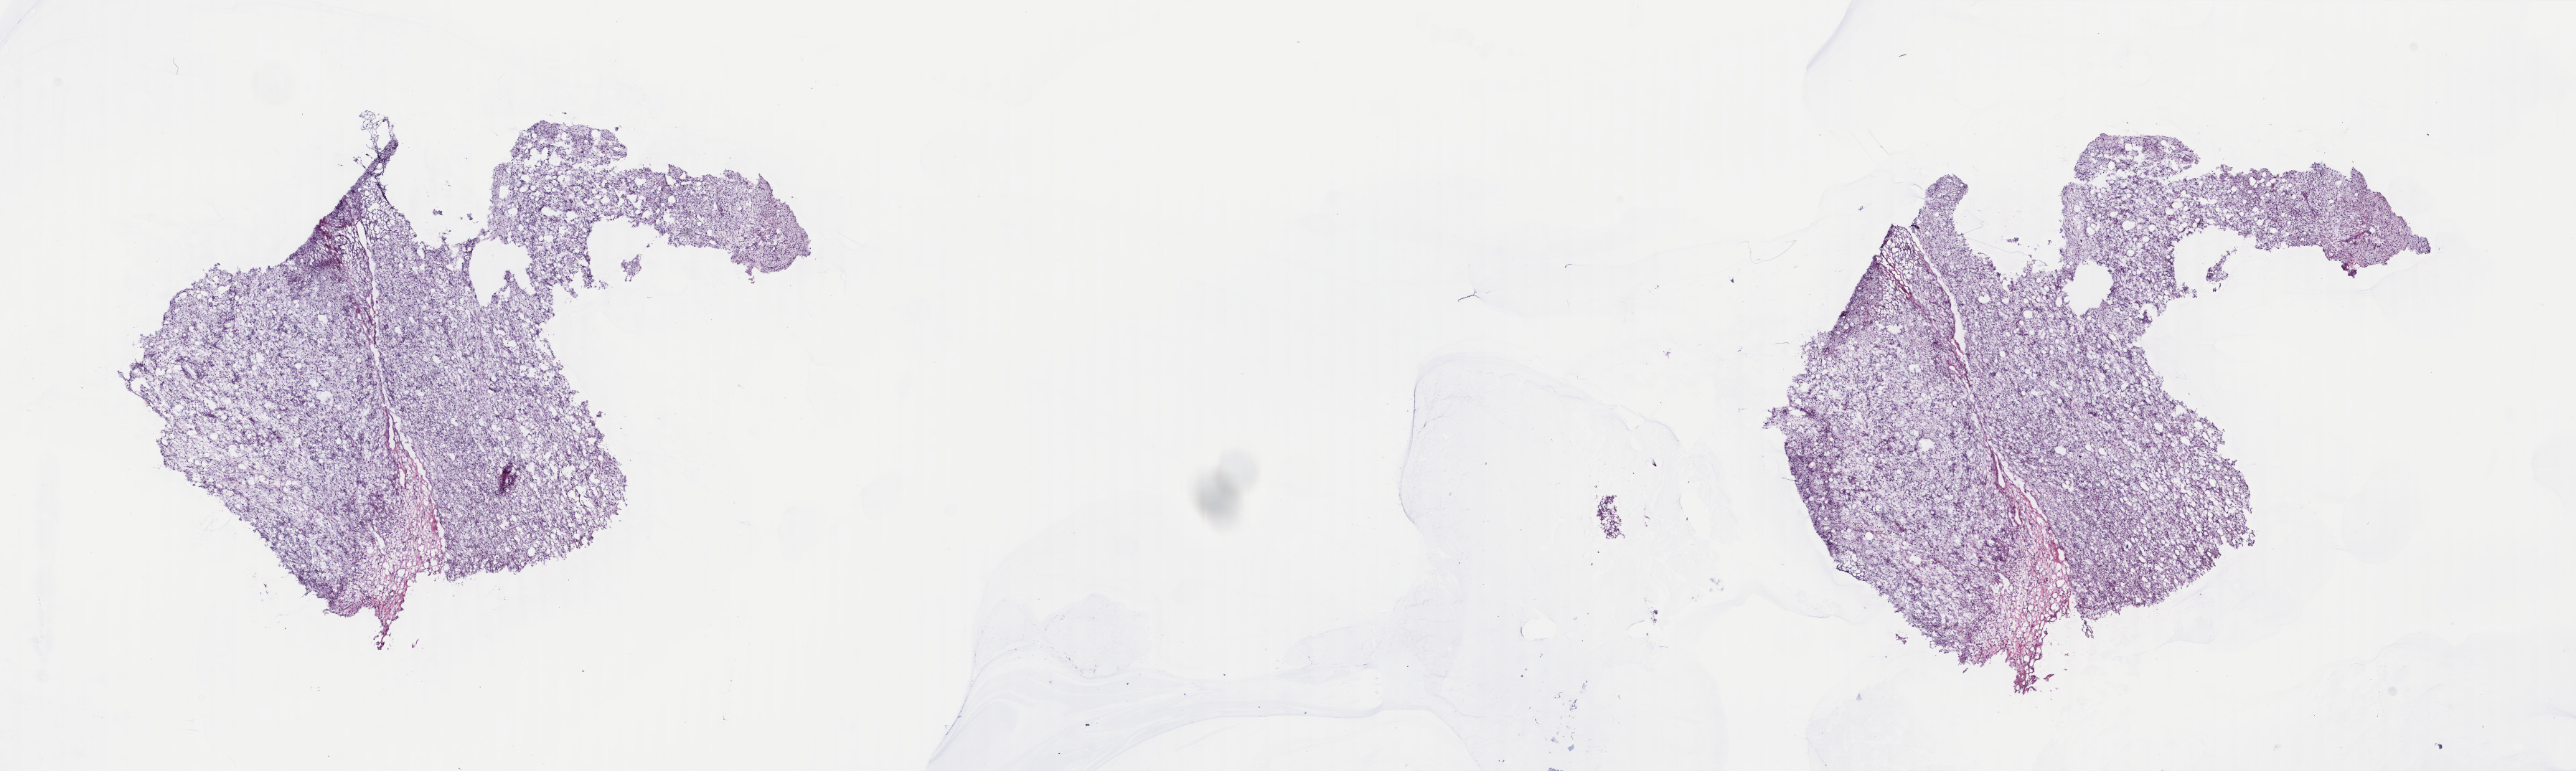
Digitized H&E-stained tissue section (whole slide) — a low-resolution overview of the entire scanned area, about 28.6 x 8.6 mm (slide scanned at 40x); frozen section from the top of the tissue portion; retroperitoneum and peritoneum, primary tumour sample. Male, age 80 years at initial diagnosis. Composition of this section per pathologist review: tumour cells 100%, tumour nuclei 90%, normal cells 0%, stromal cells 0%, necrosis 0%. Inflammatory infiltration, as recorded: lymphocyte infiltration 0%, monocyte infiltration 0%, neutrophil infiltration 0%.
Diagnosis: Dedifferentiated liposarcoma (retroperitoneum).